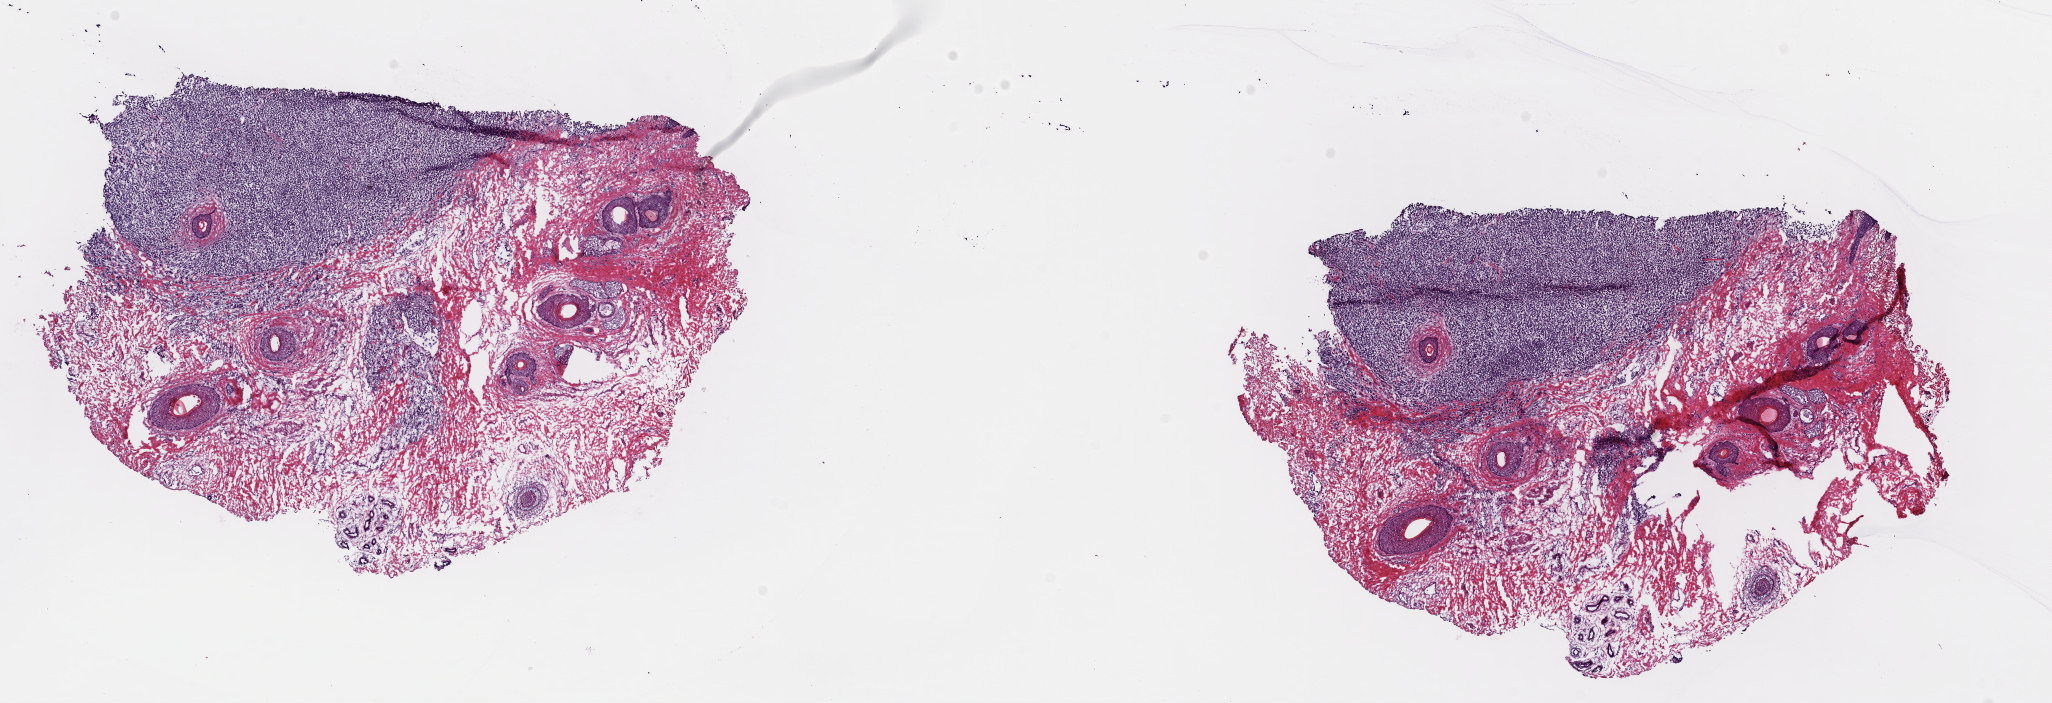
Whole-slide histology image, H&E-stained — whole scanned area (about 16.2 x 5.6 mm, slide scanned at 40x) shown as a low-resolution overview; frozen section from the top of the tissue portion; metastatic tumour sample, sampled site: lymph node. Male, age 36 years at initial diagnosis. Pathologist review of this section (percent, as recorded): tumour cells 35%, tumour nuclei 65%, normal cells 65%, stromal cells 0%, necrosis 0%. Inflammatory infiltration, as recorded: lymphocyte infiltration 0%, monocyte infiltration 0%, neutrophil infiltration 0%.
• this section: metastatic tumour tissue
• patient diagnosis: Malignant melanoma, NOS